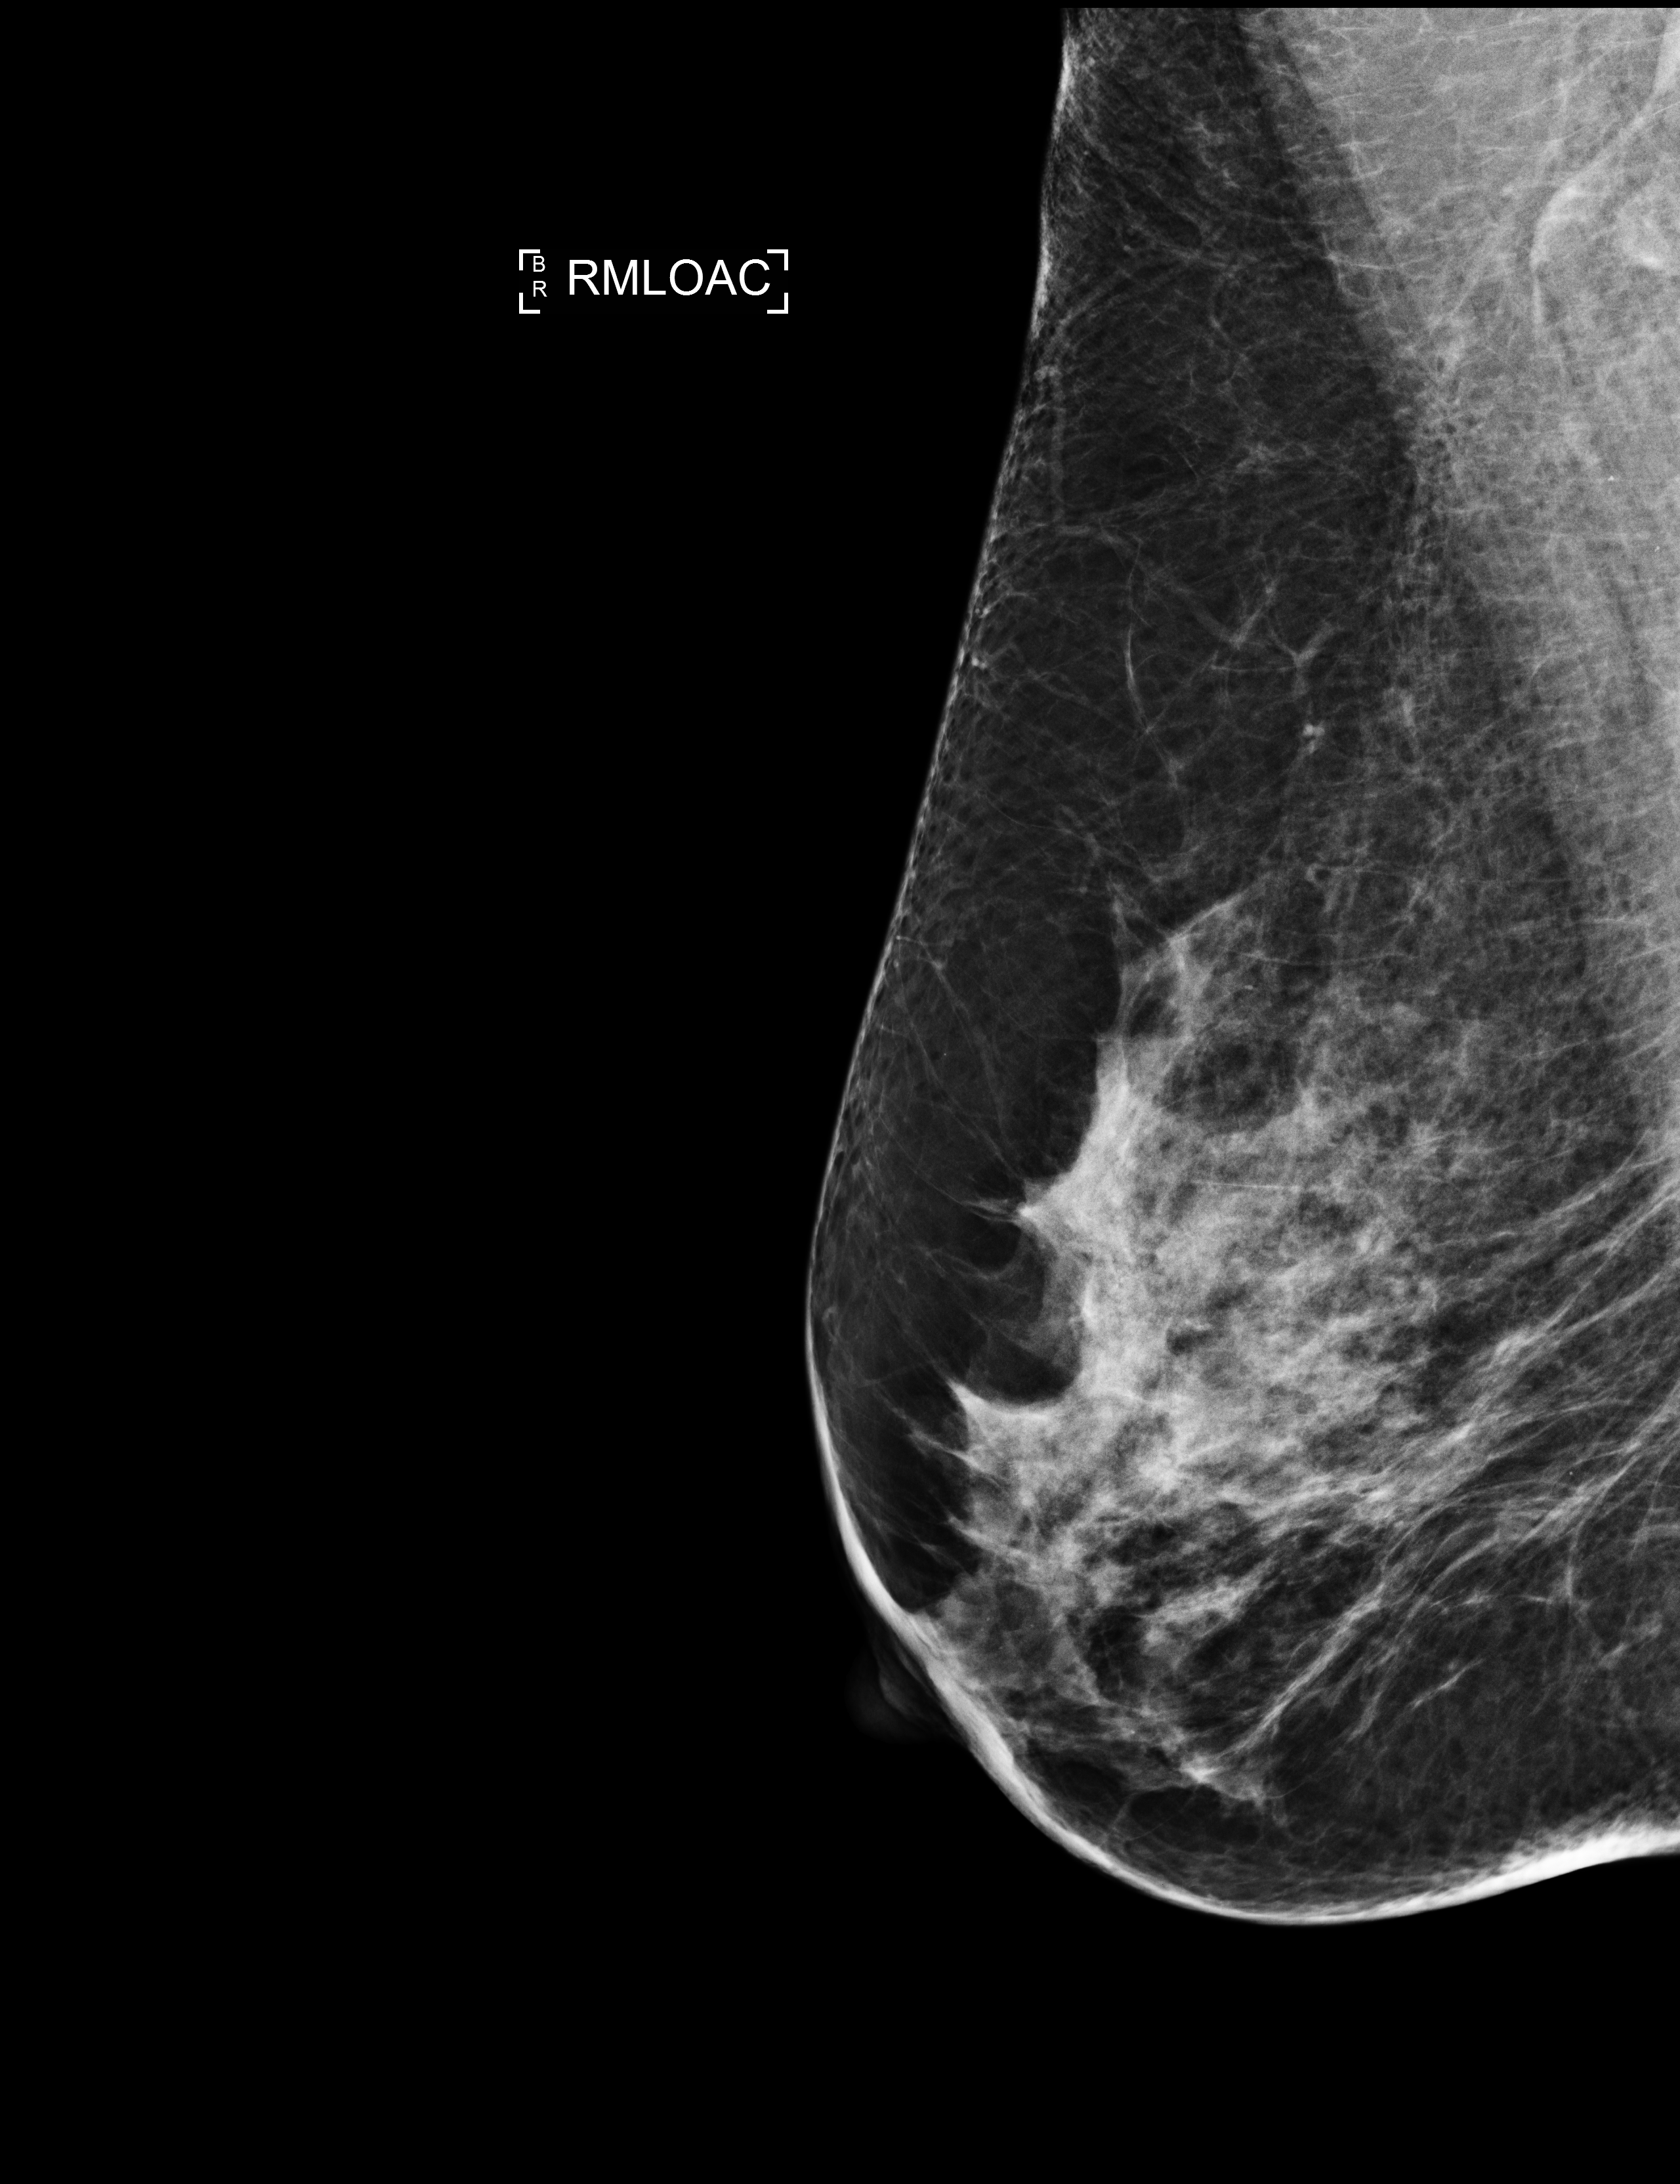
Annual screening mammography examination; system: Selenia Dimensions. Patient aged 56 years (female).
Image type: full-field digital mammogram. Breast: right. Projection: medio-lateral oblique projection, anterior compression.